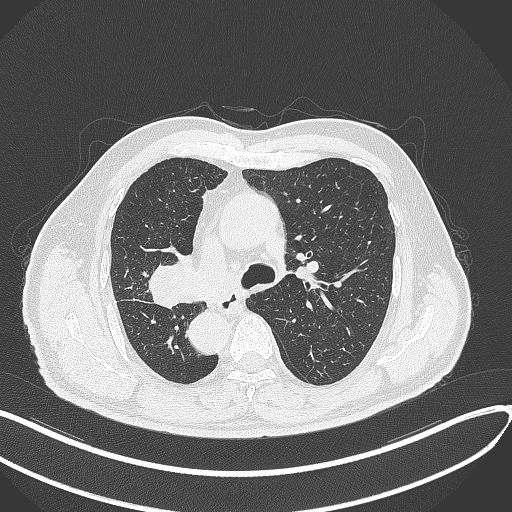
Chest CT, one axial slice. Reconstruction kernel B70f. Lung window (W 1500 / L -600 HU). 512 × 512 image matrix, field of view 400 × 400 mm. Patient: male, 67 years. From the clinical record (not read from this slice): clinical TNM (as recorded): T2a N0 M0.
Structures marked on this image (rectangle marked by the reading radiologist):
- lung tumour (recorded histology: squamous cell carcinoma): bounding box (x1, y1, x2, y2) in pixels: (146, 256, 194, 309)